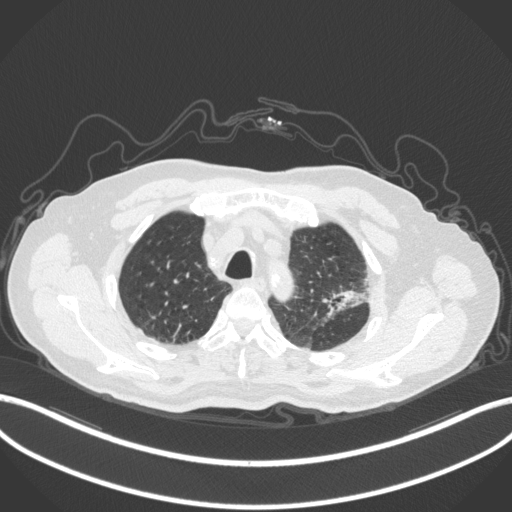
Chest CT, one axial slice. Position 246 of 331 along the scan axis. Reconstruction kernel B31f. Lung window (W 1500 / L -600 HU). 512 × 512 image matrix, field of view 400 × 400 mm. Male patient, age 79 years. From the clinical record (not read from this slice): clinical TNM (as recorded): T2a N1 M1; histopathological grade: G3.
Structures marked on this image (bounding box drawn by a radiologist):
- lung tumour (recorded histology: adenocarcinoma): bounding box <313,279,376,321> (left, top, right, bottom; pixels)